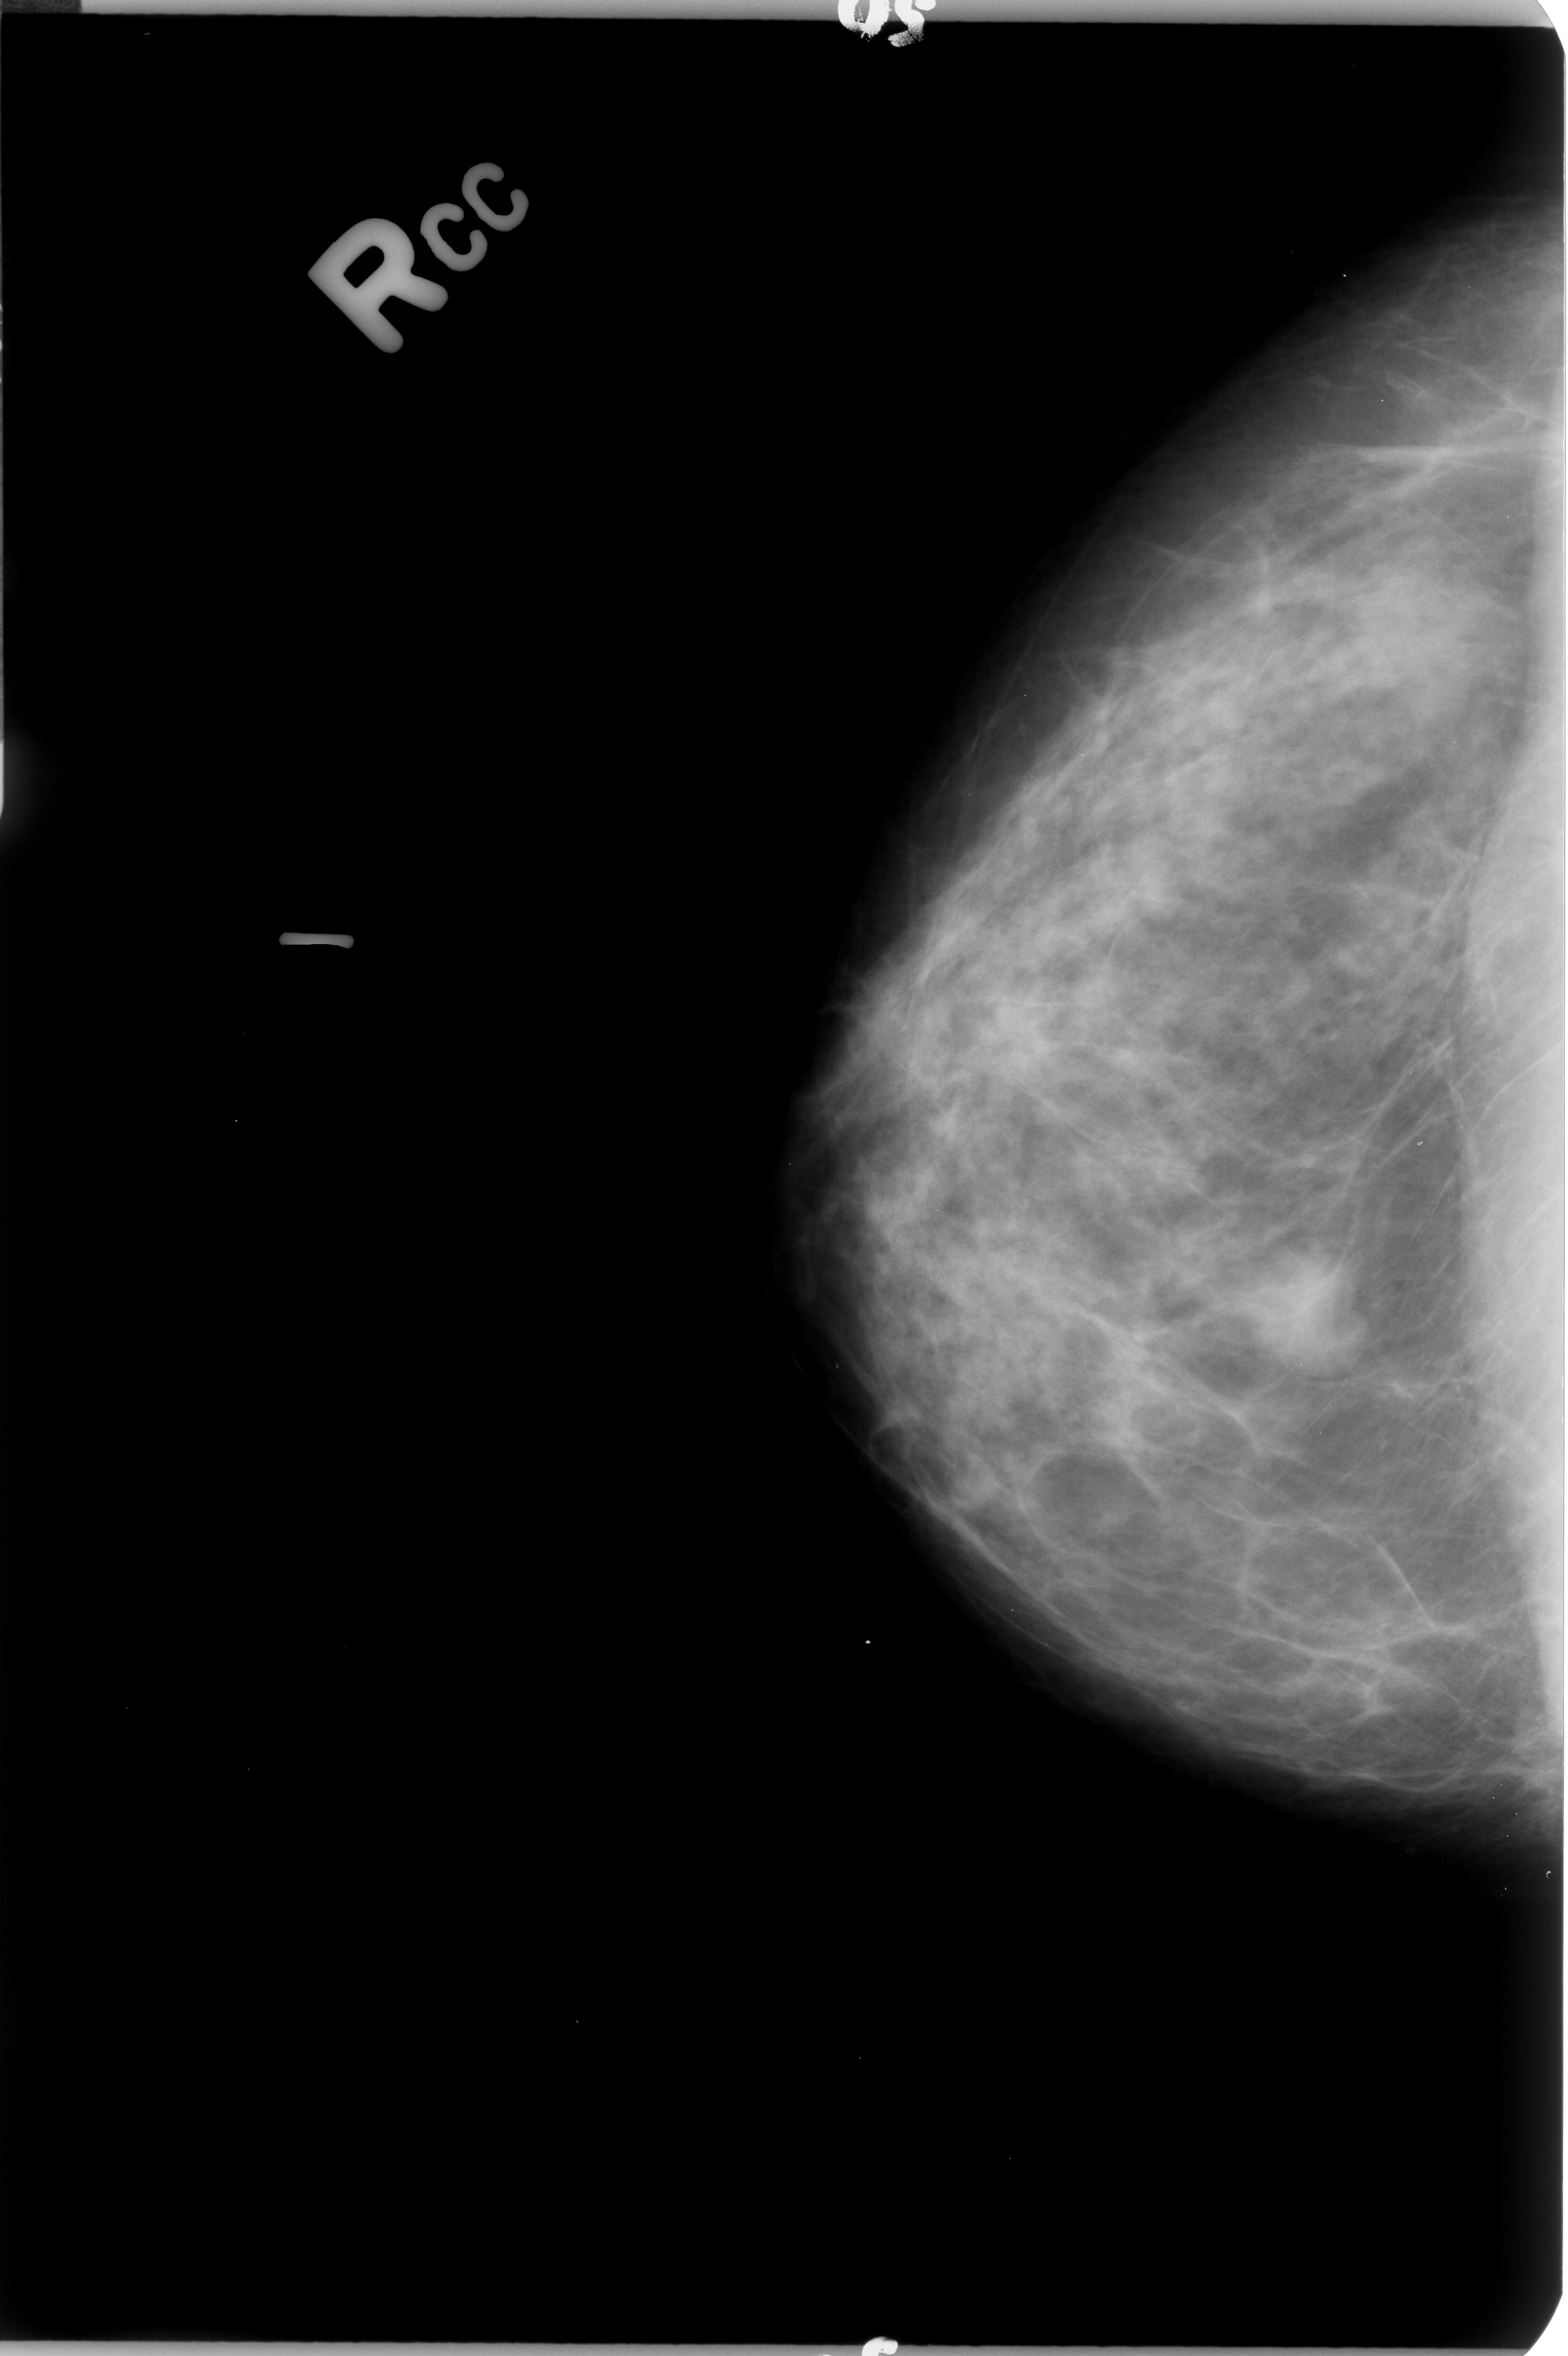
Mammogram (digitized film); right breast; CC view; breast composition: heterogeneously dense (BI-RADS density category 3 of 4); 1568 × 2356 image matrix.
Expert-marked regions of interest on this image (one box per marked abnormality):
- mass, shape lobulated, margins circumscribed / ill defined; BI-RADS assessment category 4; subtlety rating 4 on a 1 (subtle) to 5 (obvious) scale; pathology (as recorded): benign: bounding box (x1, y1, x2, y2) in pixels: (1271, 1276, 1332, 1351)